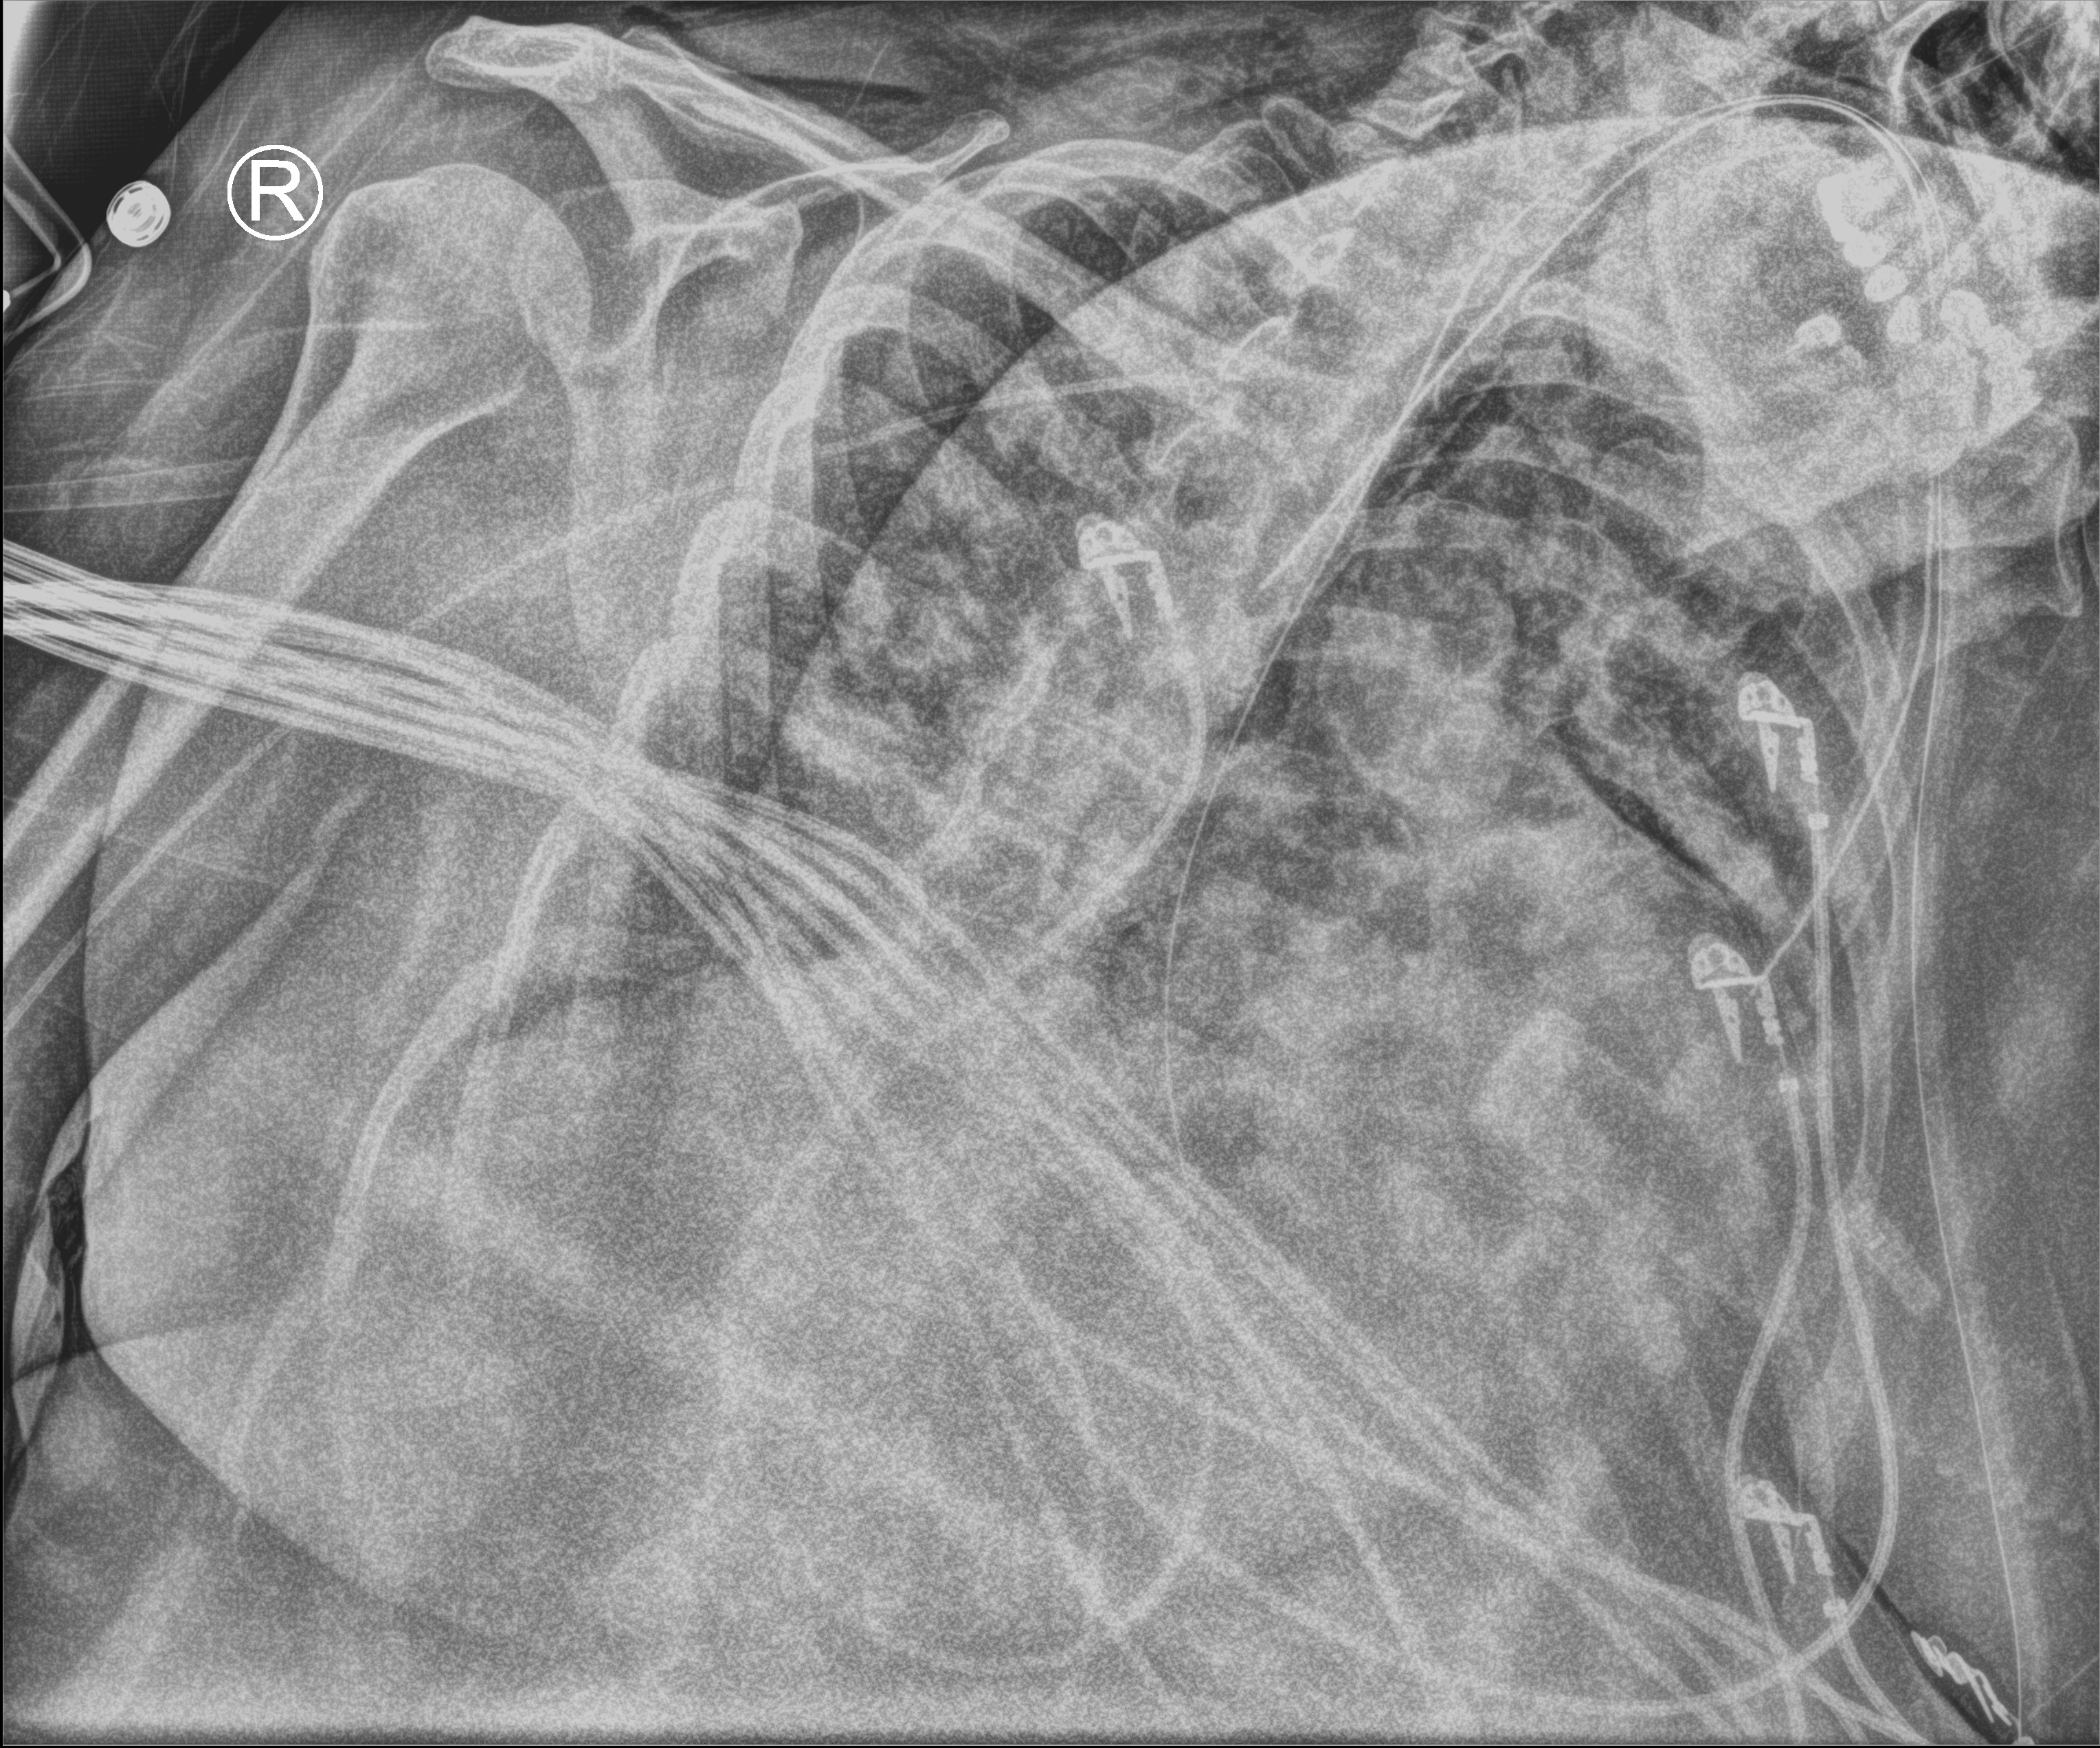
Bedside chest radiograph (computed radiography), anteroposterior (AP) projection. Female patient hospitalised with COVID-19, age 60–74 years.
From the hospital-stay record, not from the radiograph (when in the stay this image was taken is not recorded): smoking status (admission record): never.